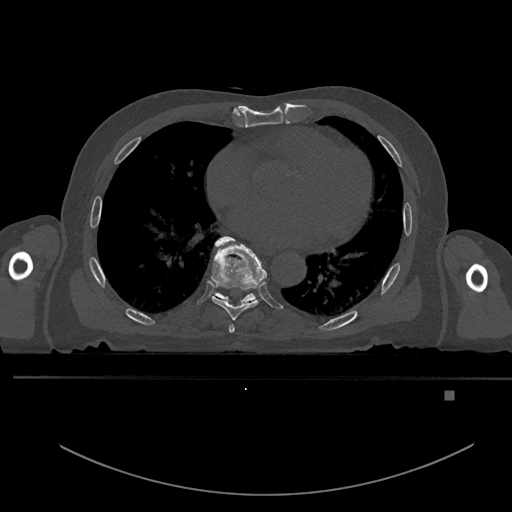
CT including the spine, one axial slice. Position 239 of 969 along the scan axis. Bone window (W 1800 / L 400 HU). 512 × 512 image matrix, field of view 456 × 456 mm. Male patient, age 82 years. From the clinical record (not read from this slice): primary cancer: prostate; vertebrae with lytic lesions (as recorded): T11, T9, T8, T2.
Outlined on this slice (semi-automatic segmentation, software-assisted and operator-edited):
- T6 vertebra: bounding box [x1, y1, x2, y2] px = [228, 324, 235, 333]
- T7 vertebra: [211, 236, 267, 321]
- T8 vertebra: [211, 241, 256, 304]